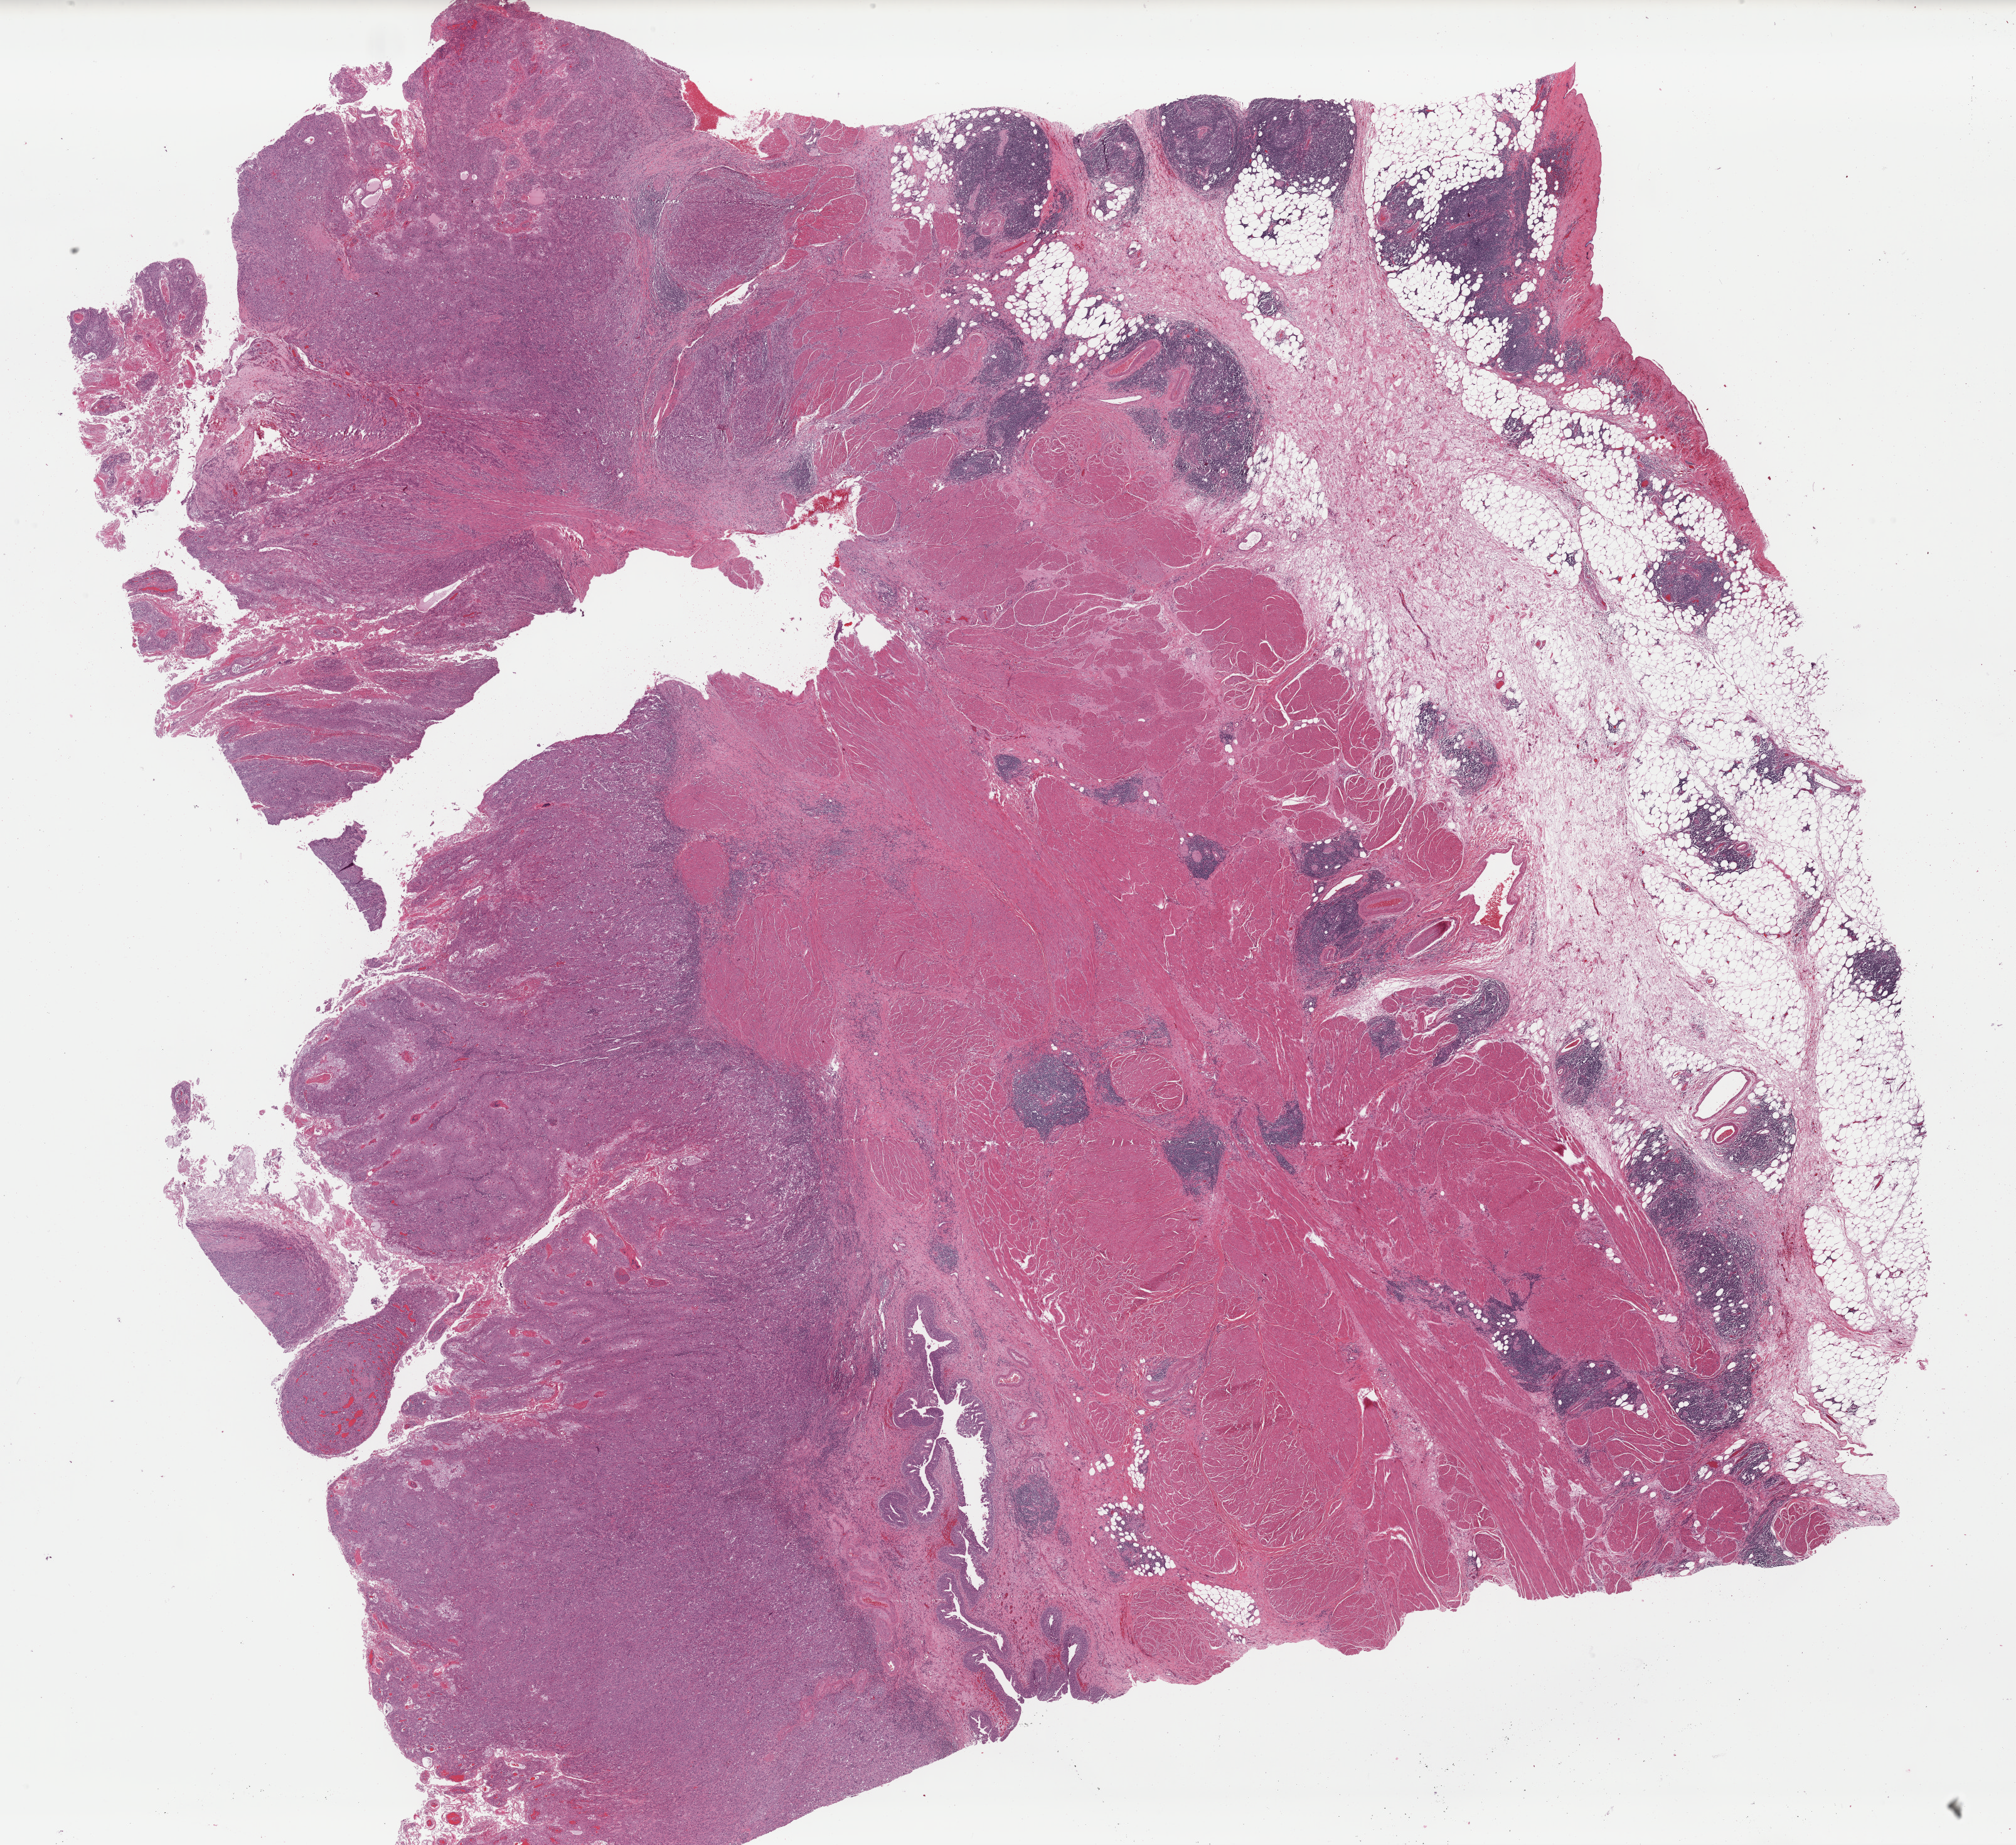
Digitized H&E tissue section (whole slide) — shown as a low-resolution overview of the whole scanned area (about 25.4 x 23.2 mm); formalin-fixed paraffin-embedded (FFPE) diagnostic section; bladder, primary tumour sample. Male, age 69 years at initial diagnosis.
Histologic diagnosis: Transitional cell carcinoma (posterior wall of bladder).